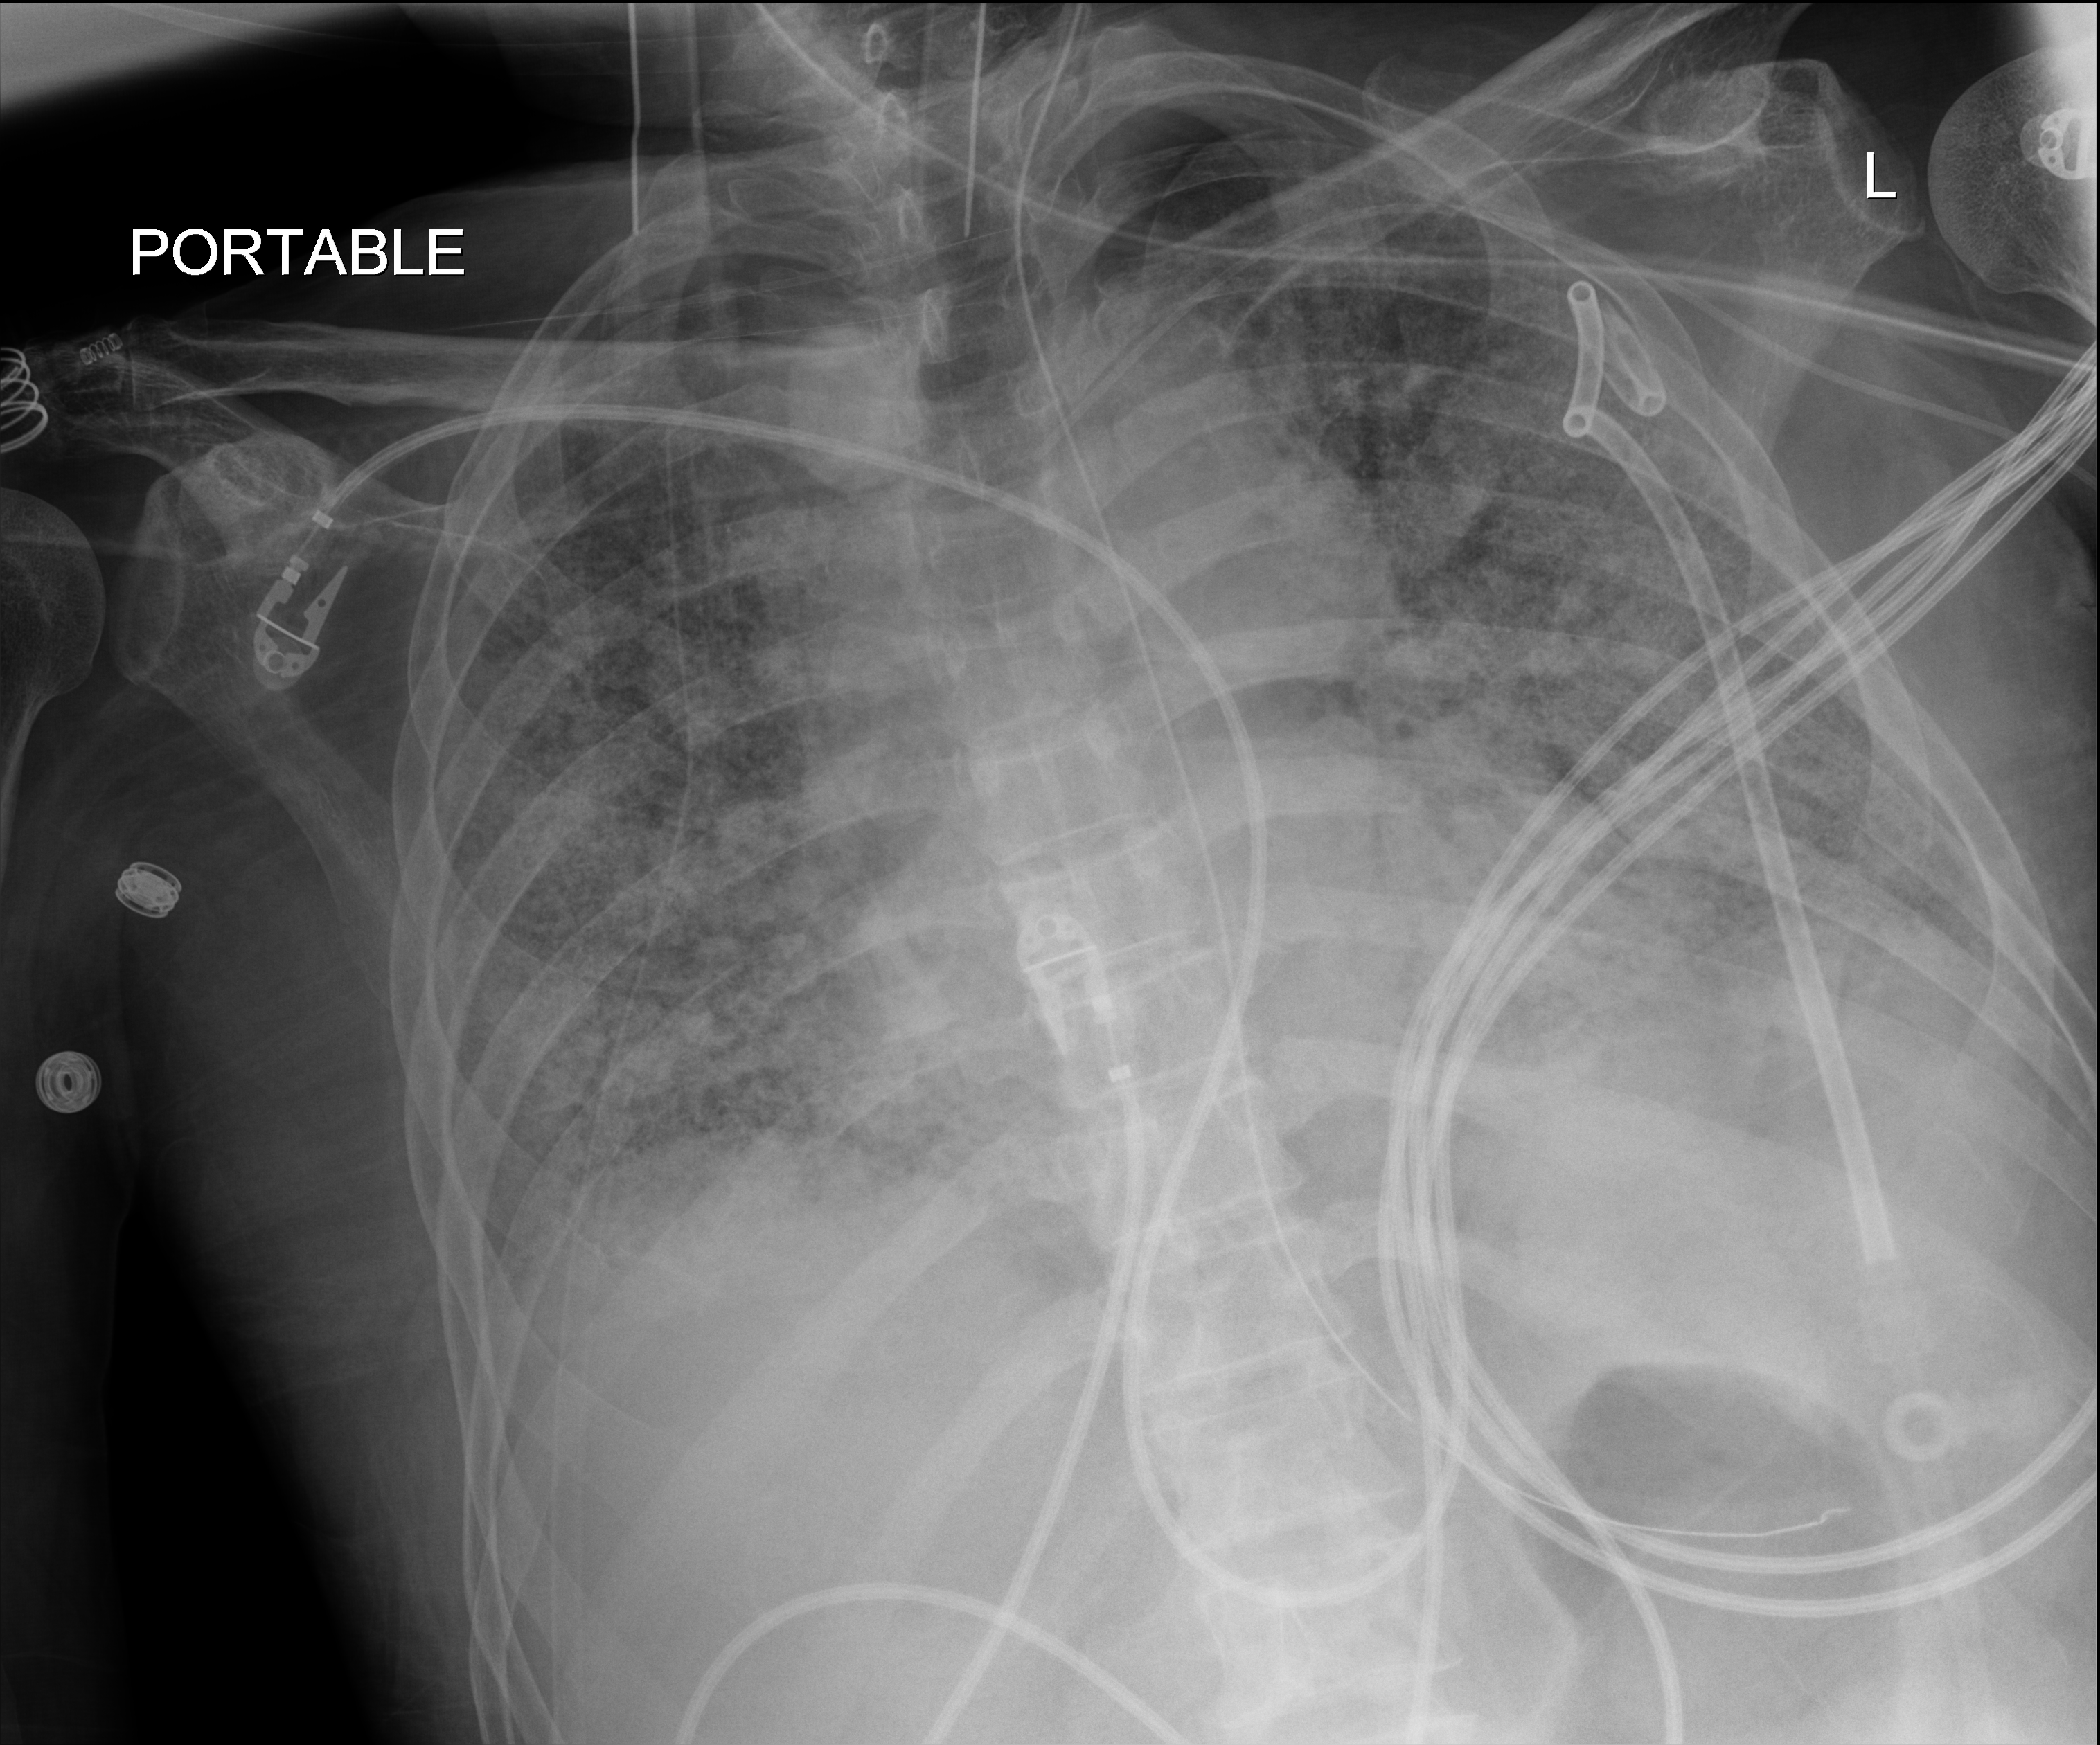
Chest X-ray (portable), anteroposterior (AP) projection. Patient hospitalised with COVID-19; male, aged 60–74 years.
Admission-level facts for this patient (not findings on this image; timing relative to this image not recorded):
- admitted to intensive care during this hospital stay: yes